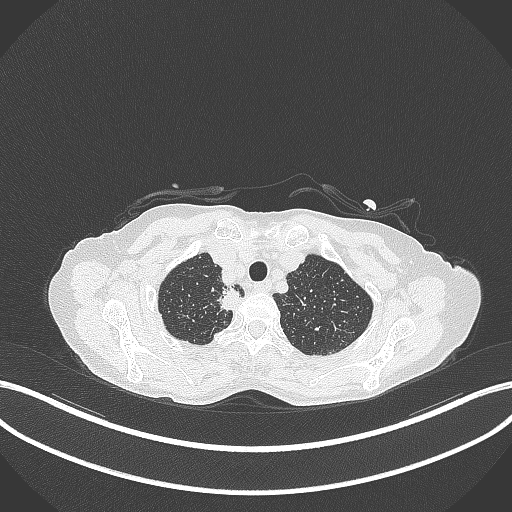
Chest CT, one axial slice. Position 327 of 403 along the scan axis. Lung window (W 1500 / L -600 HU). 1 mm slice thickness. 512 × 512 image matrix, field of view 400 × 400 mm. Patient: female, 75 years. From the clinical record (not read from this slice): clinical TNM (as recorded): T1c N1 M1.
Outlined on this slice (bounding box drawn by a radiologist):
- lung tumour (recorded histology: adenocarcinoma): box from (x=215, y=286) to (x=245, y=315) px